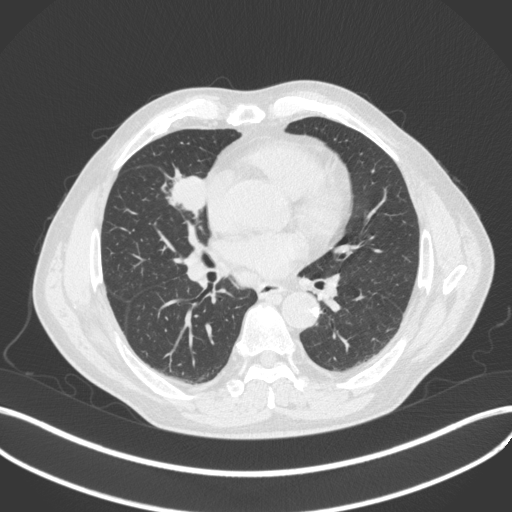
Chest CT, one axial slice; reconstruction kernel B31f; 120 kVp; lung window (W 1500 / L -600 HU); 1 mm slice thickness; 512 × 512 image matrix, field of view 400 × 400 mm. Patient: male, 61 years. Case-level facts recorded for this patient, not image findings: clinical TNM (as recorded): T2b N1 M0.
Structures marked on this image (rectangle marked by the reading radiologist):
- lung tumour (recorded histology: squamous cell carcinoma): bounding box <166,168,208,220> (left, top, right, bottom; pixels)